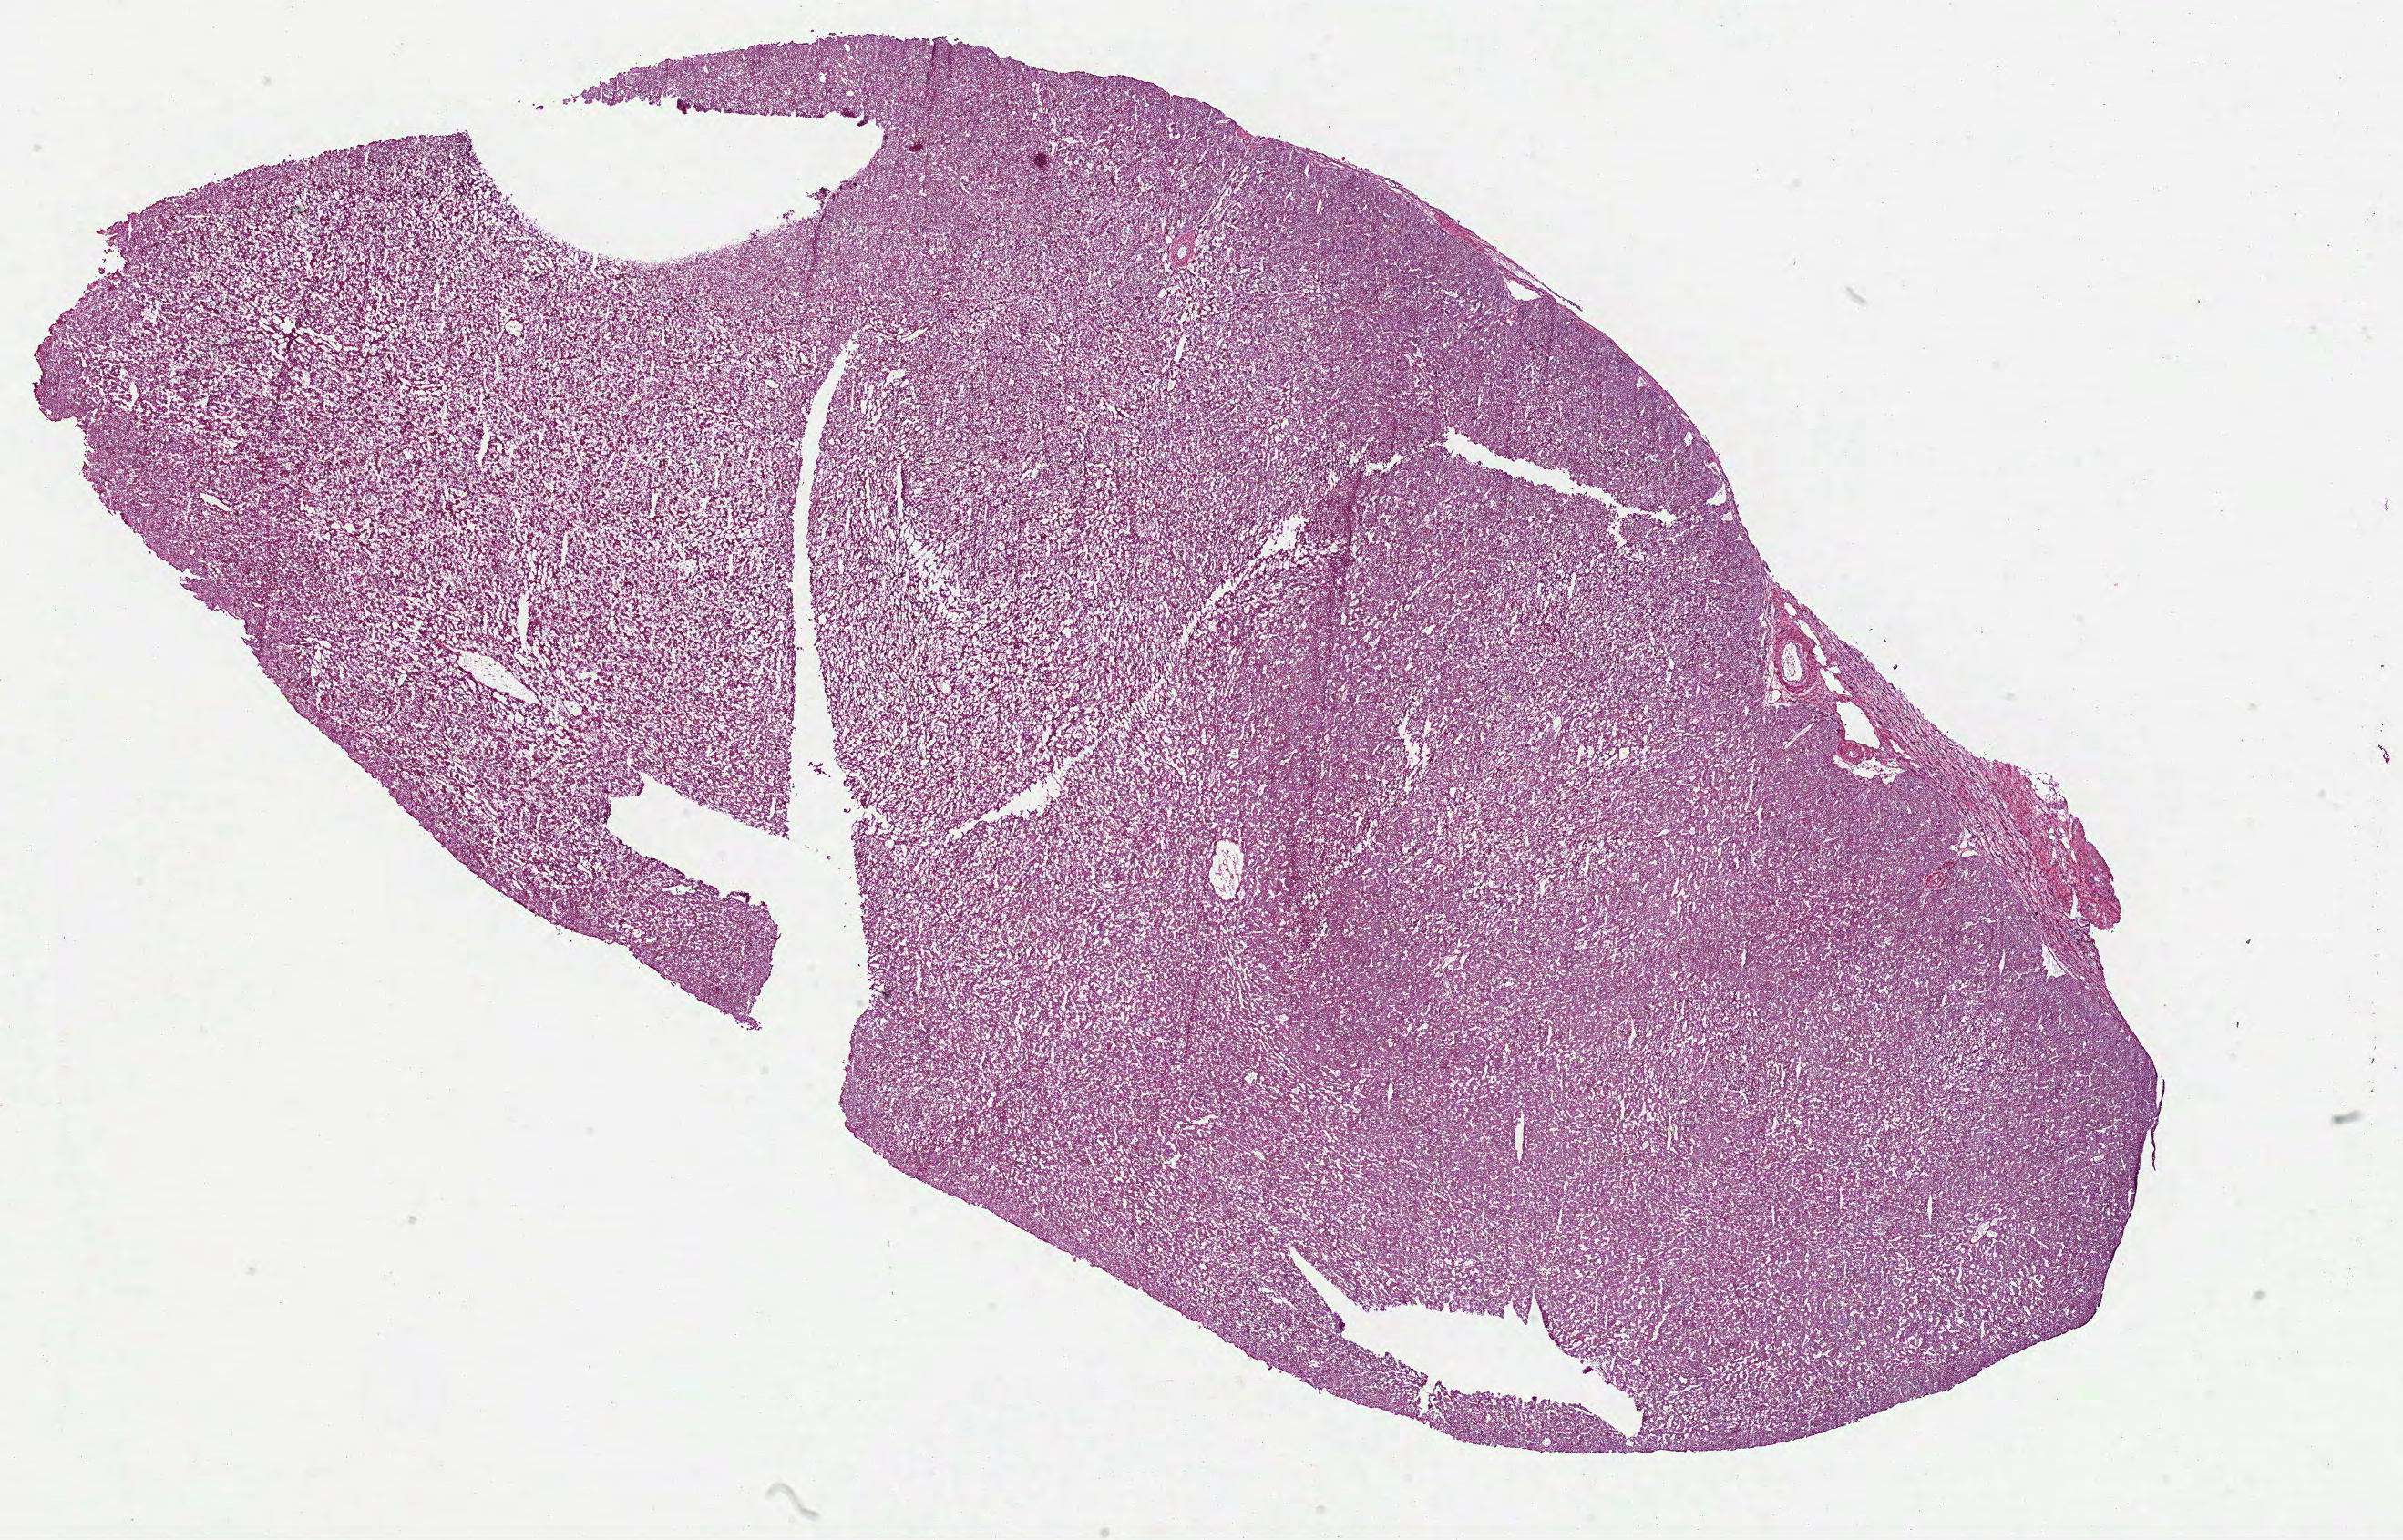
H&E whole-slide image, whole scanned area (about 21.3 x 13.6 mm, slide scanned at 40x) shown as a low-resolution overview; frozen section from the bottom of the tissue portion; primary tumour sample from the kidney. Female patient; age at initial diagnosis 42 years. Slide review estimates, as recorded: tumour cells 100%, tumour nuclei 95%, normal cells 0%, stromal cells 0%, necrosis 0%. Infiltration values recorded for this section: lymphocyte infiltration 0%, monocyte infiltration 0%, neutrophil infiltration 0%.
* AJCC pathologic stage: I
* pathologic diagnosis: Renal cell carcinoma, chromophobe type